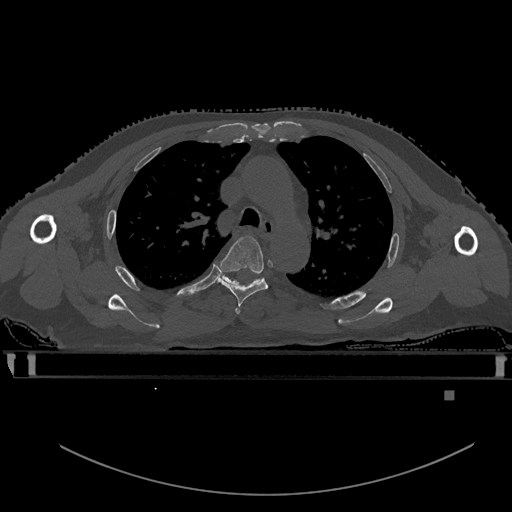
CT including the spine, one axial slice. Position 398 of 969 along the scan axis. Bone window (W 1800 / L 400 HU). 0.5 mm slice thickness. 512 × 512 image matrix. Patient: male, 82 years. Case-level facts recorded for this patient, not image findings: primary cancer: prostate; vertebrae with lytic lesions (as recorded): T11, T9, T8, T2.
Annotated regions visible in this slice (semi-automatic segmentation, software-assisted and operator-edited):
- T3 vertebra: bounding box <235,308,240,314> (left, top, right, bottom; pixels)
- T4 vertebra: <218,235,268,309>
- T5 vertebra: <218,272,262,285>